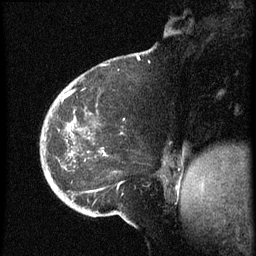
Breast MRI (dynamic contrast-enhanced), one sagittal slice. Slice 18 of 60 in the series (ordered by position). Dynamic contrast-enhanced series, image 2 of 3 at this slice position (ordered by acquisition). 1.5 T. TE 4.2 ms, TR 8.4 ms. 2.5 mm slice thickness. 256 × 256 image matrix. Female patient, age 38 years. From the clinical record (not read from this slice): setting: breast cancer imaged before/during neoadjuvant chemotherapy; receptor status: HER2-positive.
Annotated regions visible in this slice (semi-automatic segmentation, software-assisted and operator-edited):
- analysis volume of interest (the breast-tissue region the enhancement analysis was run in; not a lesion): bounding box (x1, y1, x2, y2) in pixels: (41, 74, 173, 202)
- tumour enhancement mask (voxels above the 70 % enhancement threshold inside the analysis volume of interest): (64, 93, 107, 157)